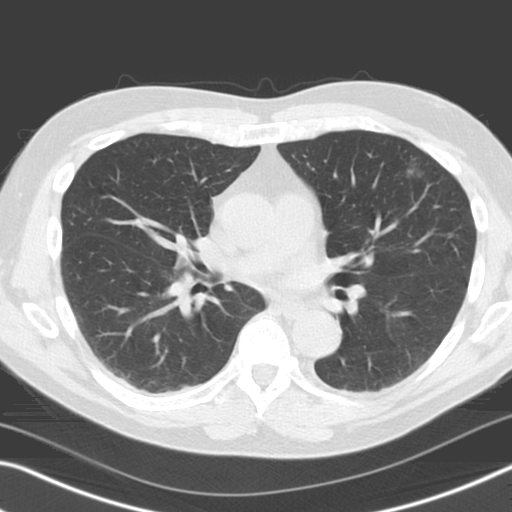
Low-dose screening chest CT, one axial slice. Slice 81 of 165 in the series (ordered by position). Lung window (W 1500 / L -600 HU). 512 × 512 image matrix.
Annotated regions visible in this slice (manually delineated by an expert):
- lesion 1 (tumor, upper lobe of left lung): bounding box [x1, y1, x2, y2] px = [405, 156, 427, 178]